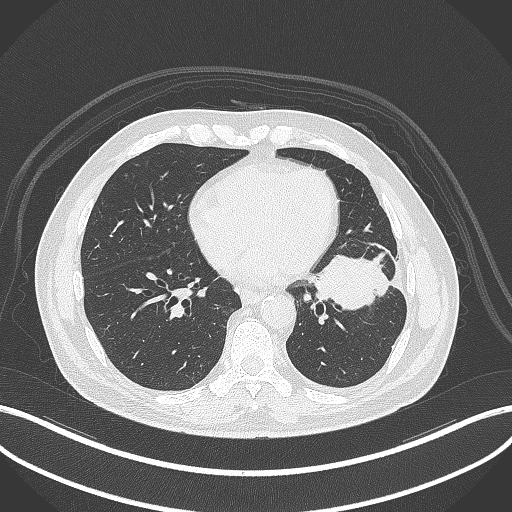
Chest CT, one axial slice; position 138 of 230 along the scan axis; 120 kVp; lung window (W 1500 / L -600 HU); 1 mm slice thickness; 512 × 512 image matrix, field of view 400 × 400 mm. Male patient, age 68 years. Case-level facts recorded for this patient, not image findings: clinical TNM (as recorded): T2b N0 M0.
Outlined on this slice (bounding box drawn by a radiologist):
- lung tumour (recorded histology: squamous cell carcinoma): bounding box (x1, y1, x2, y2) in pixels: (312, 250, 394, 313)